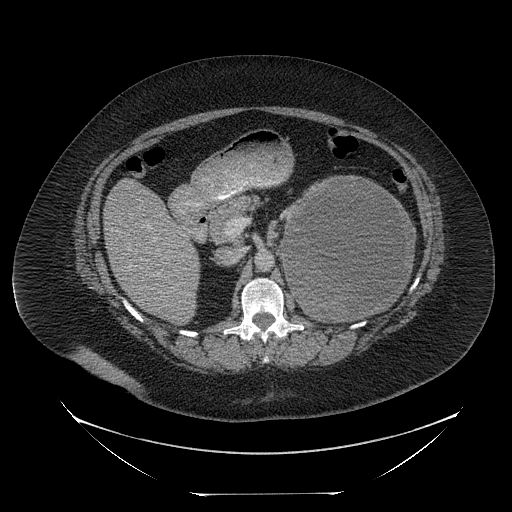
Contrast-enhanced abdominal CT, one axial slice. Position 136 of 205 along the scan axis. Reconstruction kernel STANDARD. 120 kVp. Intravenous contrast given. Soft-tissue window (W 400 / L 40 HU). 2.5 mm slice thickness. 512 × 512 image matrix. Female patient, age 53 years. Case-level facts recorded for this patient, not image findings: diagnosis: adrenocortical carcinoma; tumour side: left adrenal; tumour size at pathology: 17 cm; Ki-67 index: 20 %; stage (as recorded): 3.
Structures marked on this image (semi-automatic segmentation, software-assisted and operator-edited):
- mass: bounding box <284,179,412,320> (left, top, right, bottom; pixels)